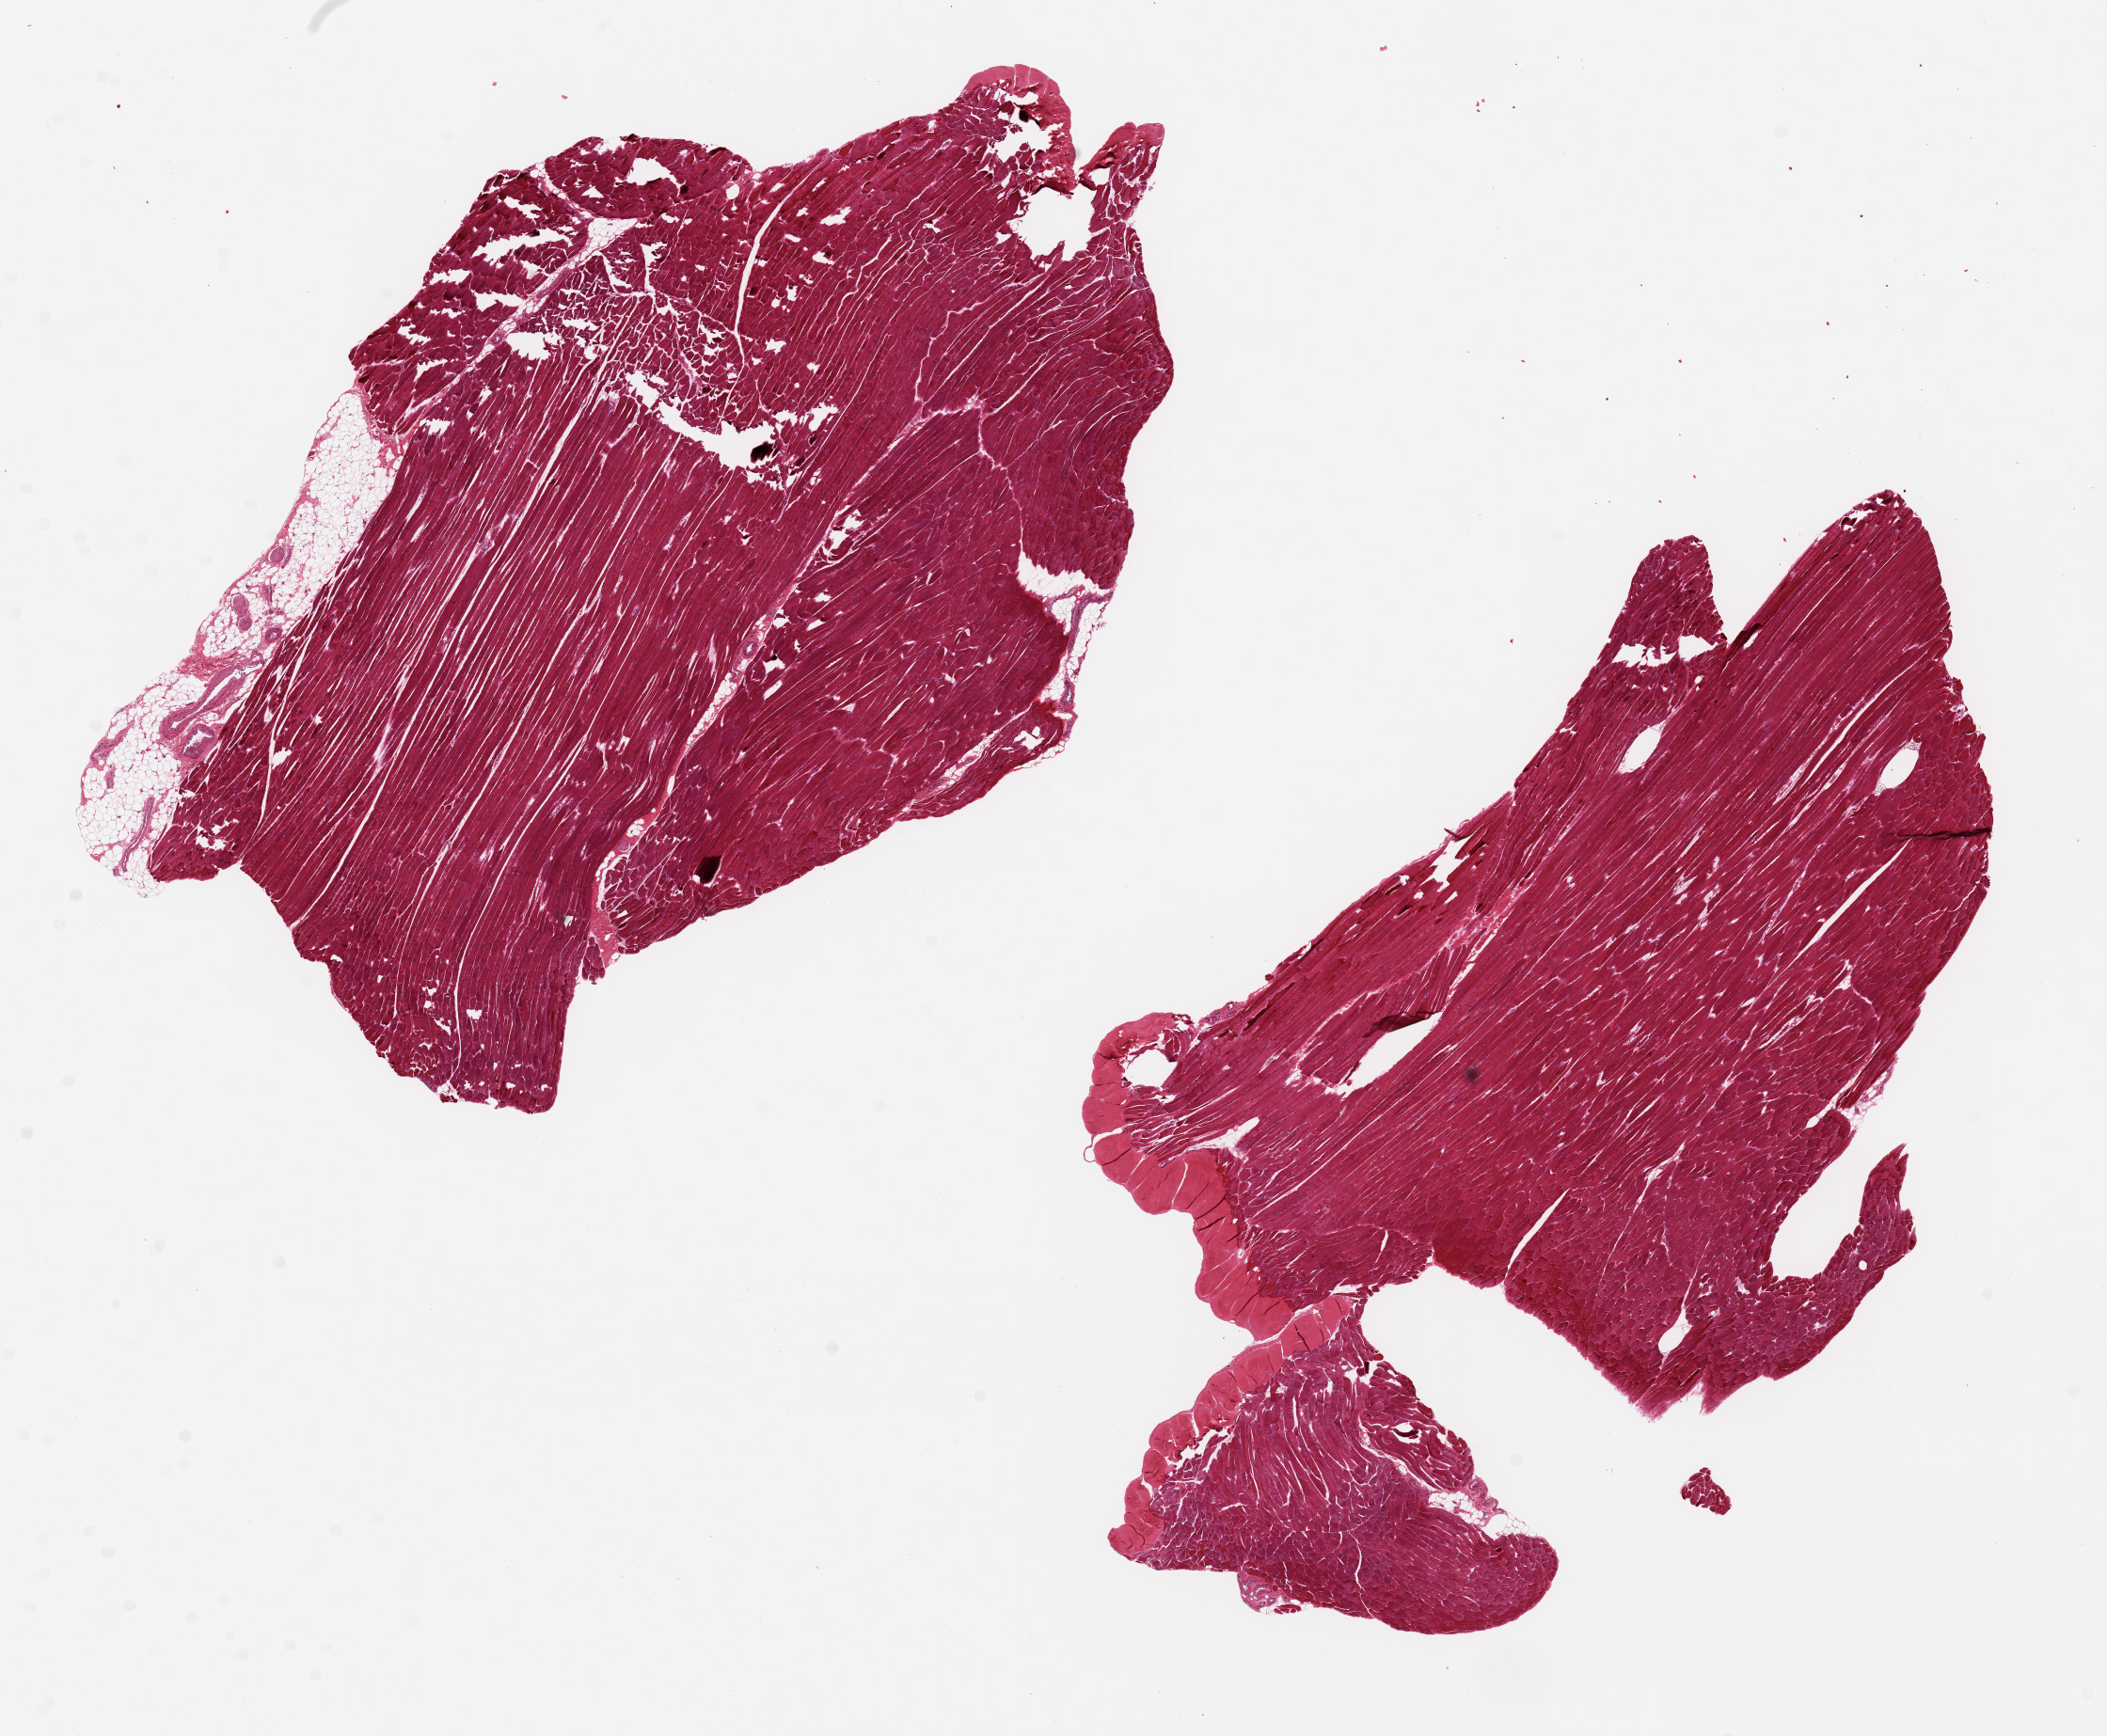
Whole-slide image, hematoxylin and eosin (H&E) stain — a low-resolution overview of the entire scanned area, about 17.7 x 14.6 mm (from a 20x scan); PAXgene-fixed paraffin-embedded (PFPE) section; section of skeletal muscle (target tissue); tissue donor sample. Donor sex: male.
Reviewer comment on this tissue sample: 2 ~10x6mm aliquots; ~5% interstitial adipose tissue in one.